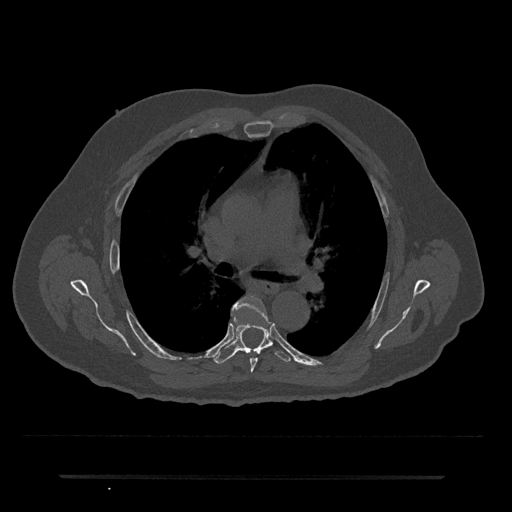
CT including the spine, one axial slice. 120 kVp. Bone window (W 1800 / L 400 HU). 512 × 512 image matrix, field of view 437 × 437 mm. Patient: male, 69 years. Case-level facts recorded for this patient, not image findings: primary cancer: prostate.
Outlined on this slice (semi-automatically segmented with operator editing):
- T5 vertebra: box from (x=233, y=296) to (x=267, y=373) px
- T6 vertebra: (x=214, y=316)–(x=291, y=364)